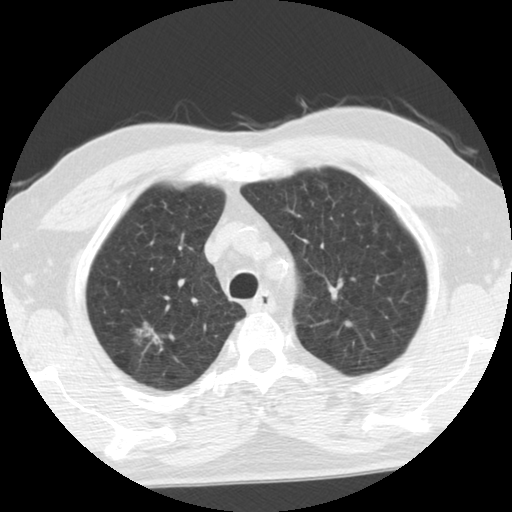
Low-dose screening chest CT, axial slice. Second annual screen. Lung window (W 1500 / L -600 HU). 2.5 mm slice thickness. 512 × 512 image matrix. Male, age 68 years at enrolment. Former smoker at enrolment.
Expert-annotated lung lesion, bounding box <129,313,169,349> (left, top, right, bottom; pixels). Reader record for this screening exam (exam-level; its link to the box is not recorded): non-calcified nodule or mass ≥4 mm, right upper lobe, poorly defined margins, ground glass attenuation, pre-existing on the prior screen: yes; interval growth: yes.